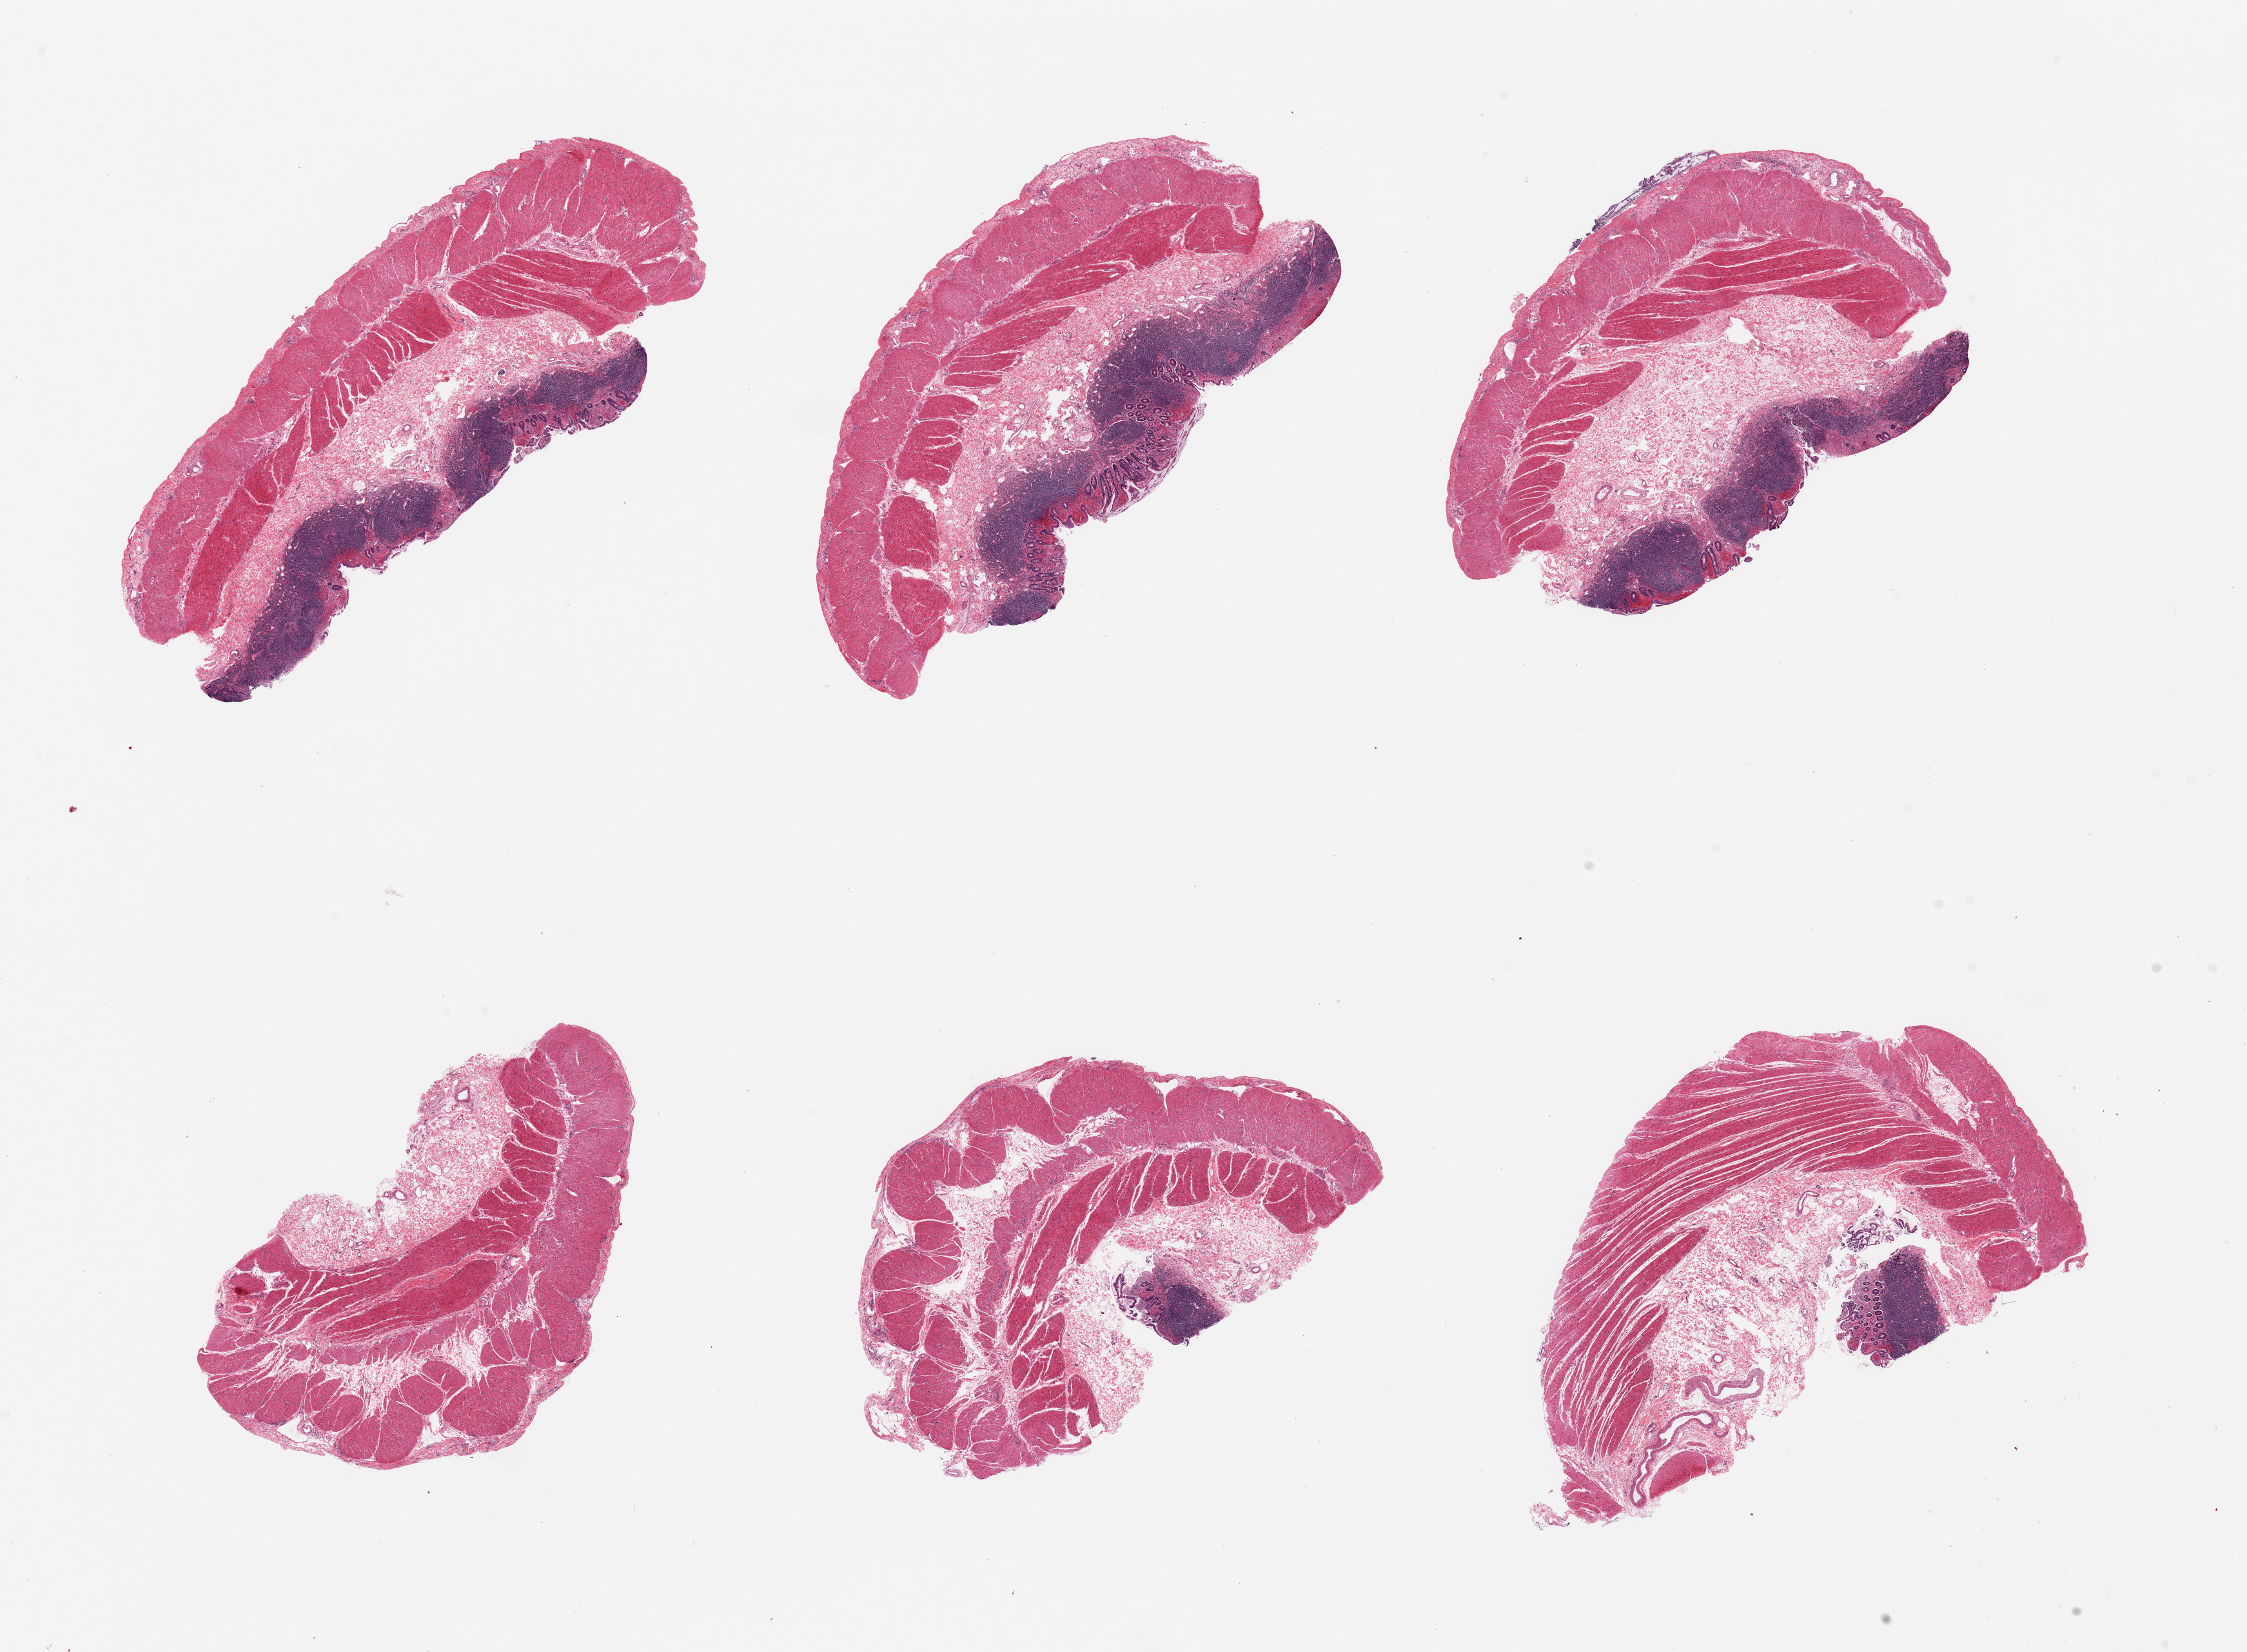
H&E whole-slide image — a low-resolution overview of the entire scanned area, about 27.6 x 20.3 mm. PAXgene-fixed paraffin-embedded (PFPE) section. Sampled site (target tissue): sigmoid colon. Donor tissue sample. Donor sex: female.
Pathologist's review note for this sample: 6 pieces, multiple pieces include mucosa (not target), mucosa contains prominent lymphoid tissue (?ileum).